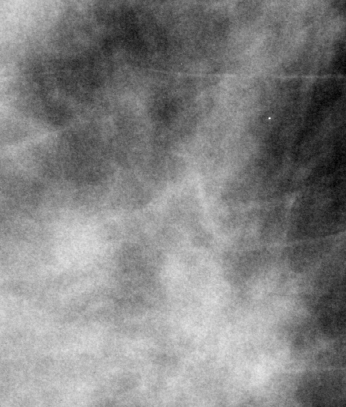
Cropped region of a digitized screen-film mammogram centred on a radiologist-marked abnormality, right breast, MLO view.
Mass, shape irregular, margins spiculated; BI-RADS assessment category 4; subtlety rating 4 on a 1 (subtle) to 5 (obvious) scale; benign; no additional work-up was recommended (benign without callback).